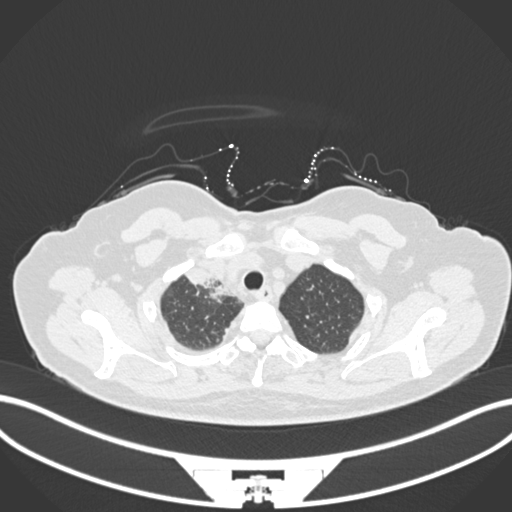
Chest CT, one axial slice. Reconstruction kernel B30f. Lung window (W 1500 / L -600 HU). 1 mm slice thickness. 512 × 512 image matrix, field of view 400 × 400 mm. Female patient, age 52 years. From the clinical record (not read from this slice): clinical TNM (as recorded): T3 N1 M1.
Structures marked on this image (bounding box drawn by a radiologist):
- lung tumour (recorded histology: adenocarcinoma): bounding box [x1, y1, x2, y2] px = [184, 265, 234, 303]